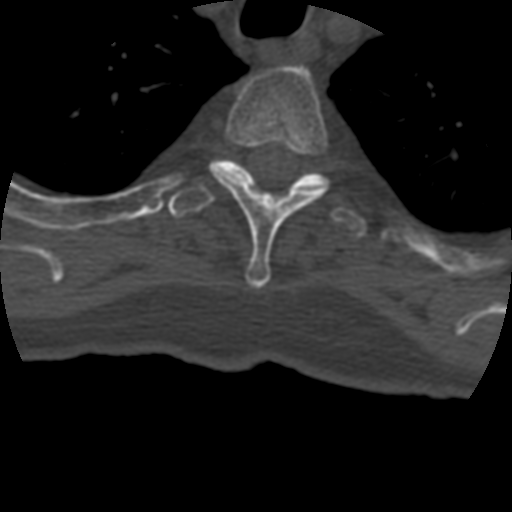
CT including the spine, one axial slice. Position 348 of 399 along the scan axis. Reconstruction kernel STANDARD. 120 kVp. Bone window (W 1800 / L 400 HU). 512 × 512 image matrix, field of view 160 × 160 mm. Patient age 69 years. Case-level facts recorded for this patient, not image findings: primary cancer: prostate.
Outlined on this slice (semi-automatic segmentation, software-assisted and operator-edited):
- T3 vertebra: bounding box [x1, y1, x2, y2] px = [209, 66, 328, 289]
- T4 vertebra: [168, 159, 368, 240]